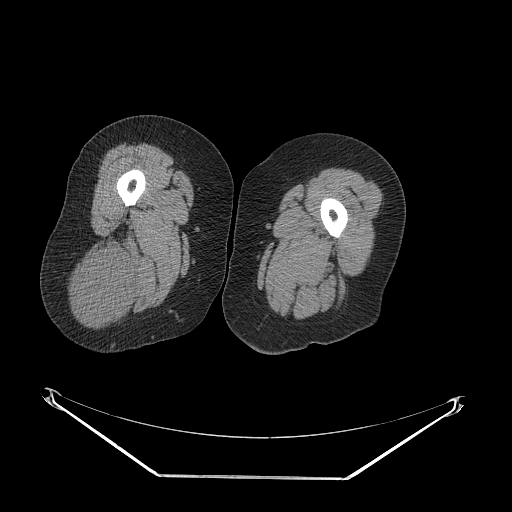
CT of an extremity soft-tissue mass (from a PET/CT study), one axial slice; position 31 of 257 along the scan axis; reconstruction kernel STANDARD; 140 kVp; soft-tissue window (W 400 / L 40 HU); 512 × 512 image matrix, field of view 500 × 500 mm. Female patient. Case-level facts recorded for this patient, not image findings: histological type: synovial sarcoma; grade: intermediate; site of the primary tumour: right buttock.
Structures marked on this image (expert contour drawn on MRI and transferred to this co-registered scan by the dataset authors):
- gross tumour volume including surrounding oedema: bounding box (x1, y1, x2, y2) in pixels: (71, 242, 134, 321)
- gross tumour volume (mass): (75, 249, 133, 321)